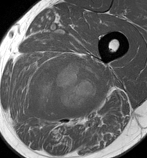
MRI of an extremity soft-tissue mass, one axial slice; slice 73 of 86 in the series (ordered by position); MR volume resampled by the dataset authors to the PET/CT grid (not the native acquisition matrix); 3.27 mm slice thickness; 147 × 158 image matrix, field of view 144 × 154 mm. Male patient. Case-level facts recorded for this patient, not image findings: histological type: undifferentiated pleomorphic liposarcoma; grade: high; site of the primary tumour: left thigh.
Outlined on this slice (expert contour drawn on MRI and transferred to this co-registered scan by the dataset authors):
- gross tumour volume including surrounding oedema: box from (x=21, y=58) to (x=109, y=127) px
- gross tumour volume (mass): (x=30, y=62)–(x=106, y=120)